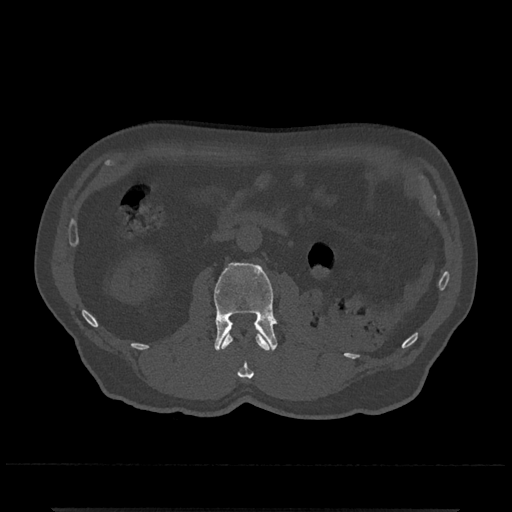
CT including the spine, one axial slice; slice 310 of 797 in the series (ordered by position); reconstruction kernel Br40s/3; bone window (W 1800 / L 400 HU); 0.5 mm slice thickness; 512 × 512 image matrix, field of view 393 × 393 mm. Male patient, age 67 years. From the clinical record (not read from this slice): primary cancer: prostate.
Annotated regions visible in this slice (semi-automatic segmentation, software-assisted and operator-edited):
- L1 vertebra: box from (x=221, y=332) to (x=270, y=378) px
- L2 vertebra: (x=214, y=262)–(x=279, y=351)